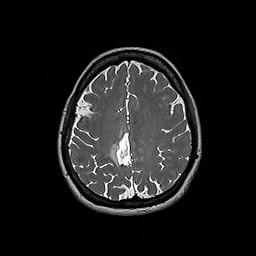
Brain MRI from a brain-tumour surgery series, one axial slice. Position 65 of 192 along the scan axis. 1 mm slice thickness. 256 × 256 image matrix, field of view 250 × 250 mm. Case-level facts recorded for this patient, not image findings: histopathology: Oligodendroglioma; WHO grade: 2; IDH mutation: yes.
Annotated regions visible in this slice (outlined manually by an expert reader):
- tumour: bounding box <110,143,120,165> (left, top, right, bottom; pixels)